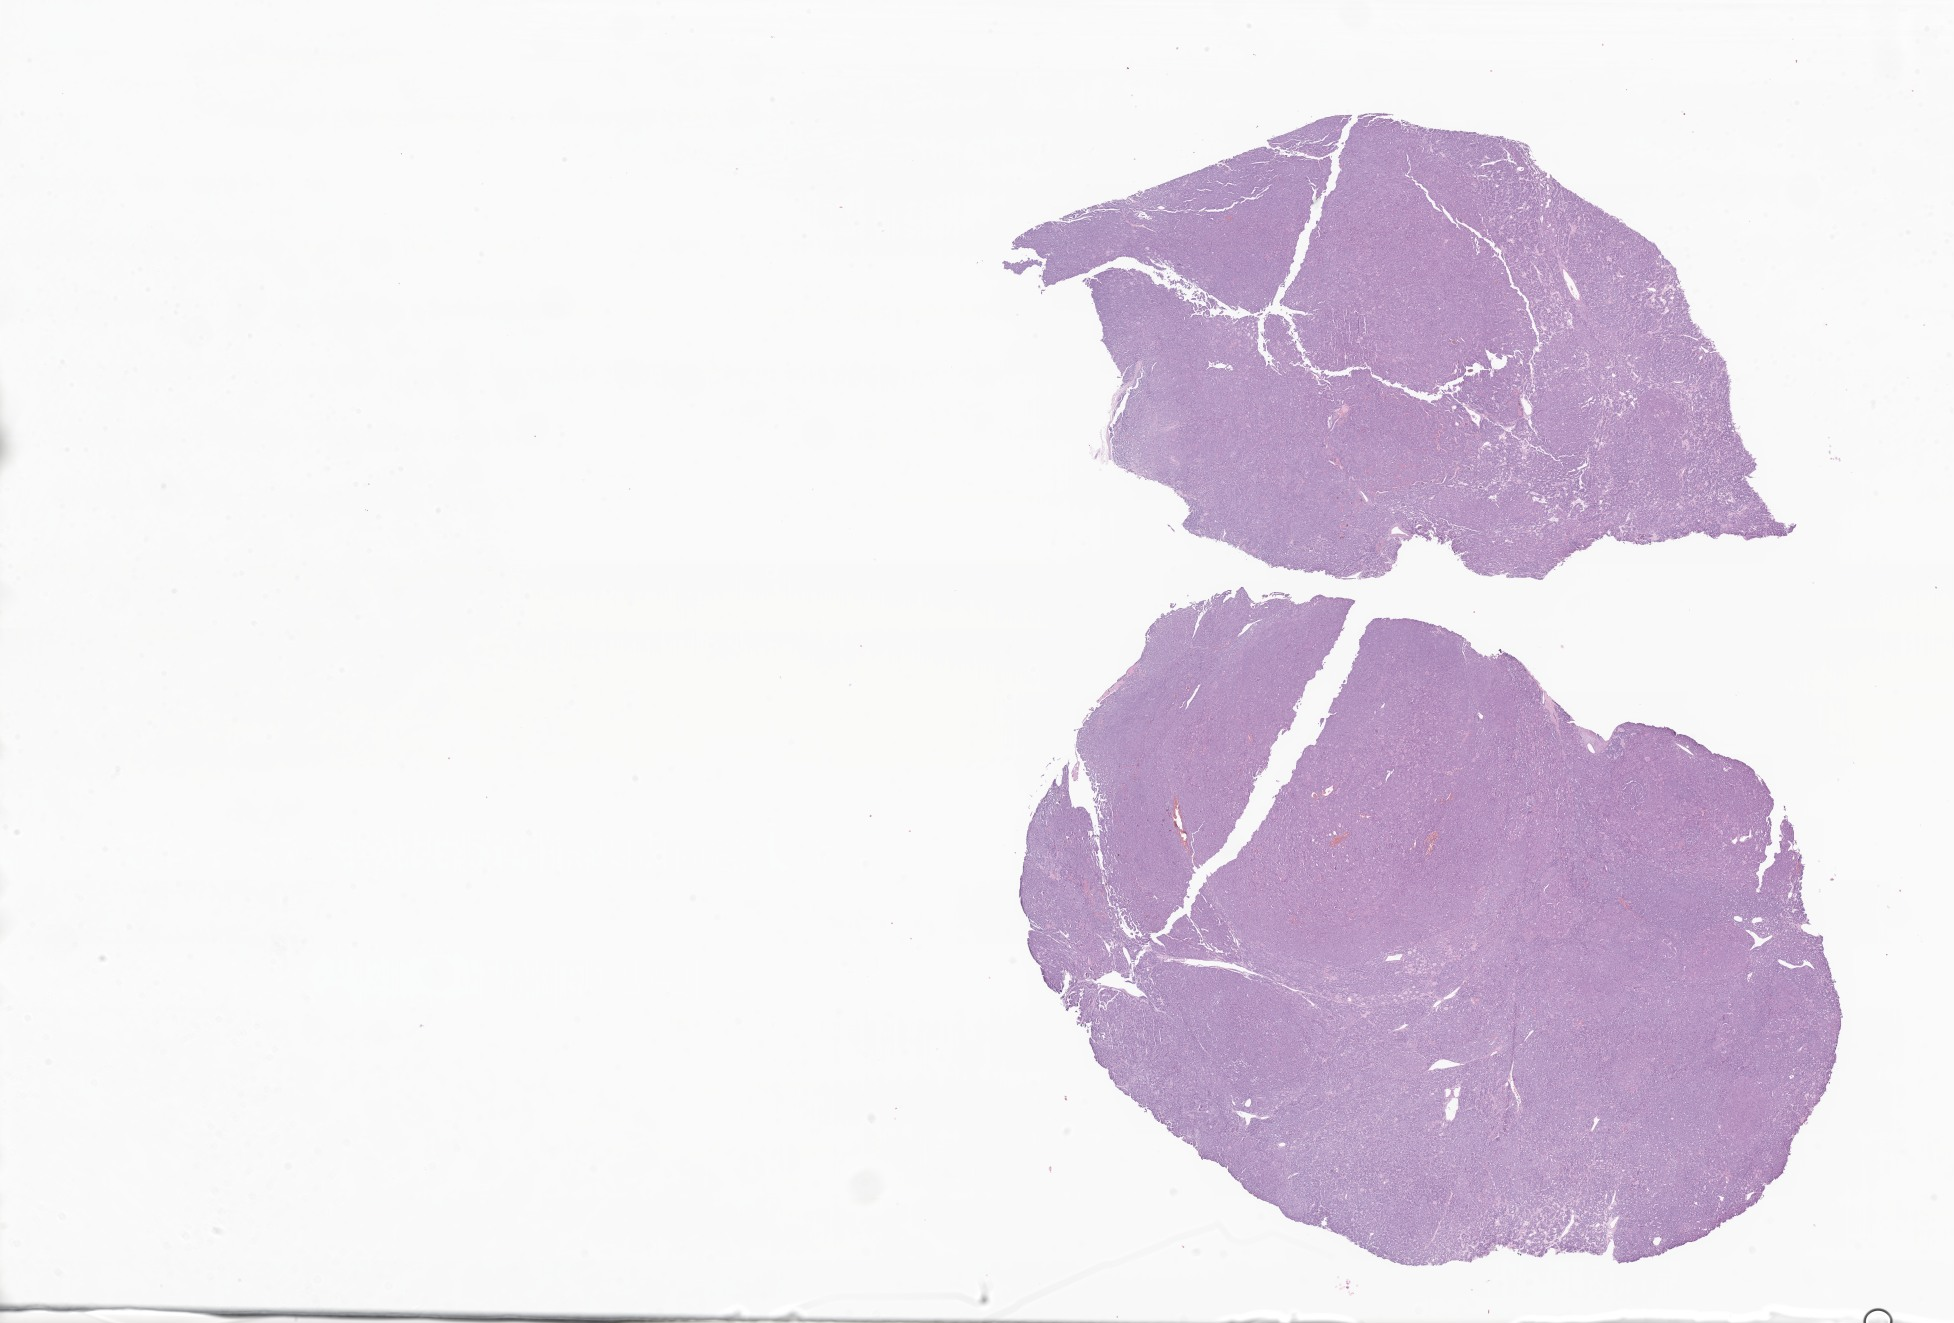
Digitized haematoxylin and eosin-stained section of tumor tissue from the thyroid — low-resolution overview of the scanned area, about 33.0 x 22.3 mm, FFPE section. Male patient, age 188 months (15 years 8 months).
• diagnosis: Papillary carcinoma, NOS